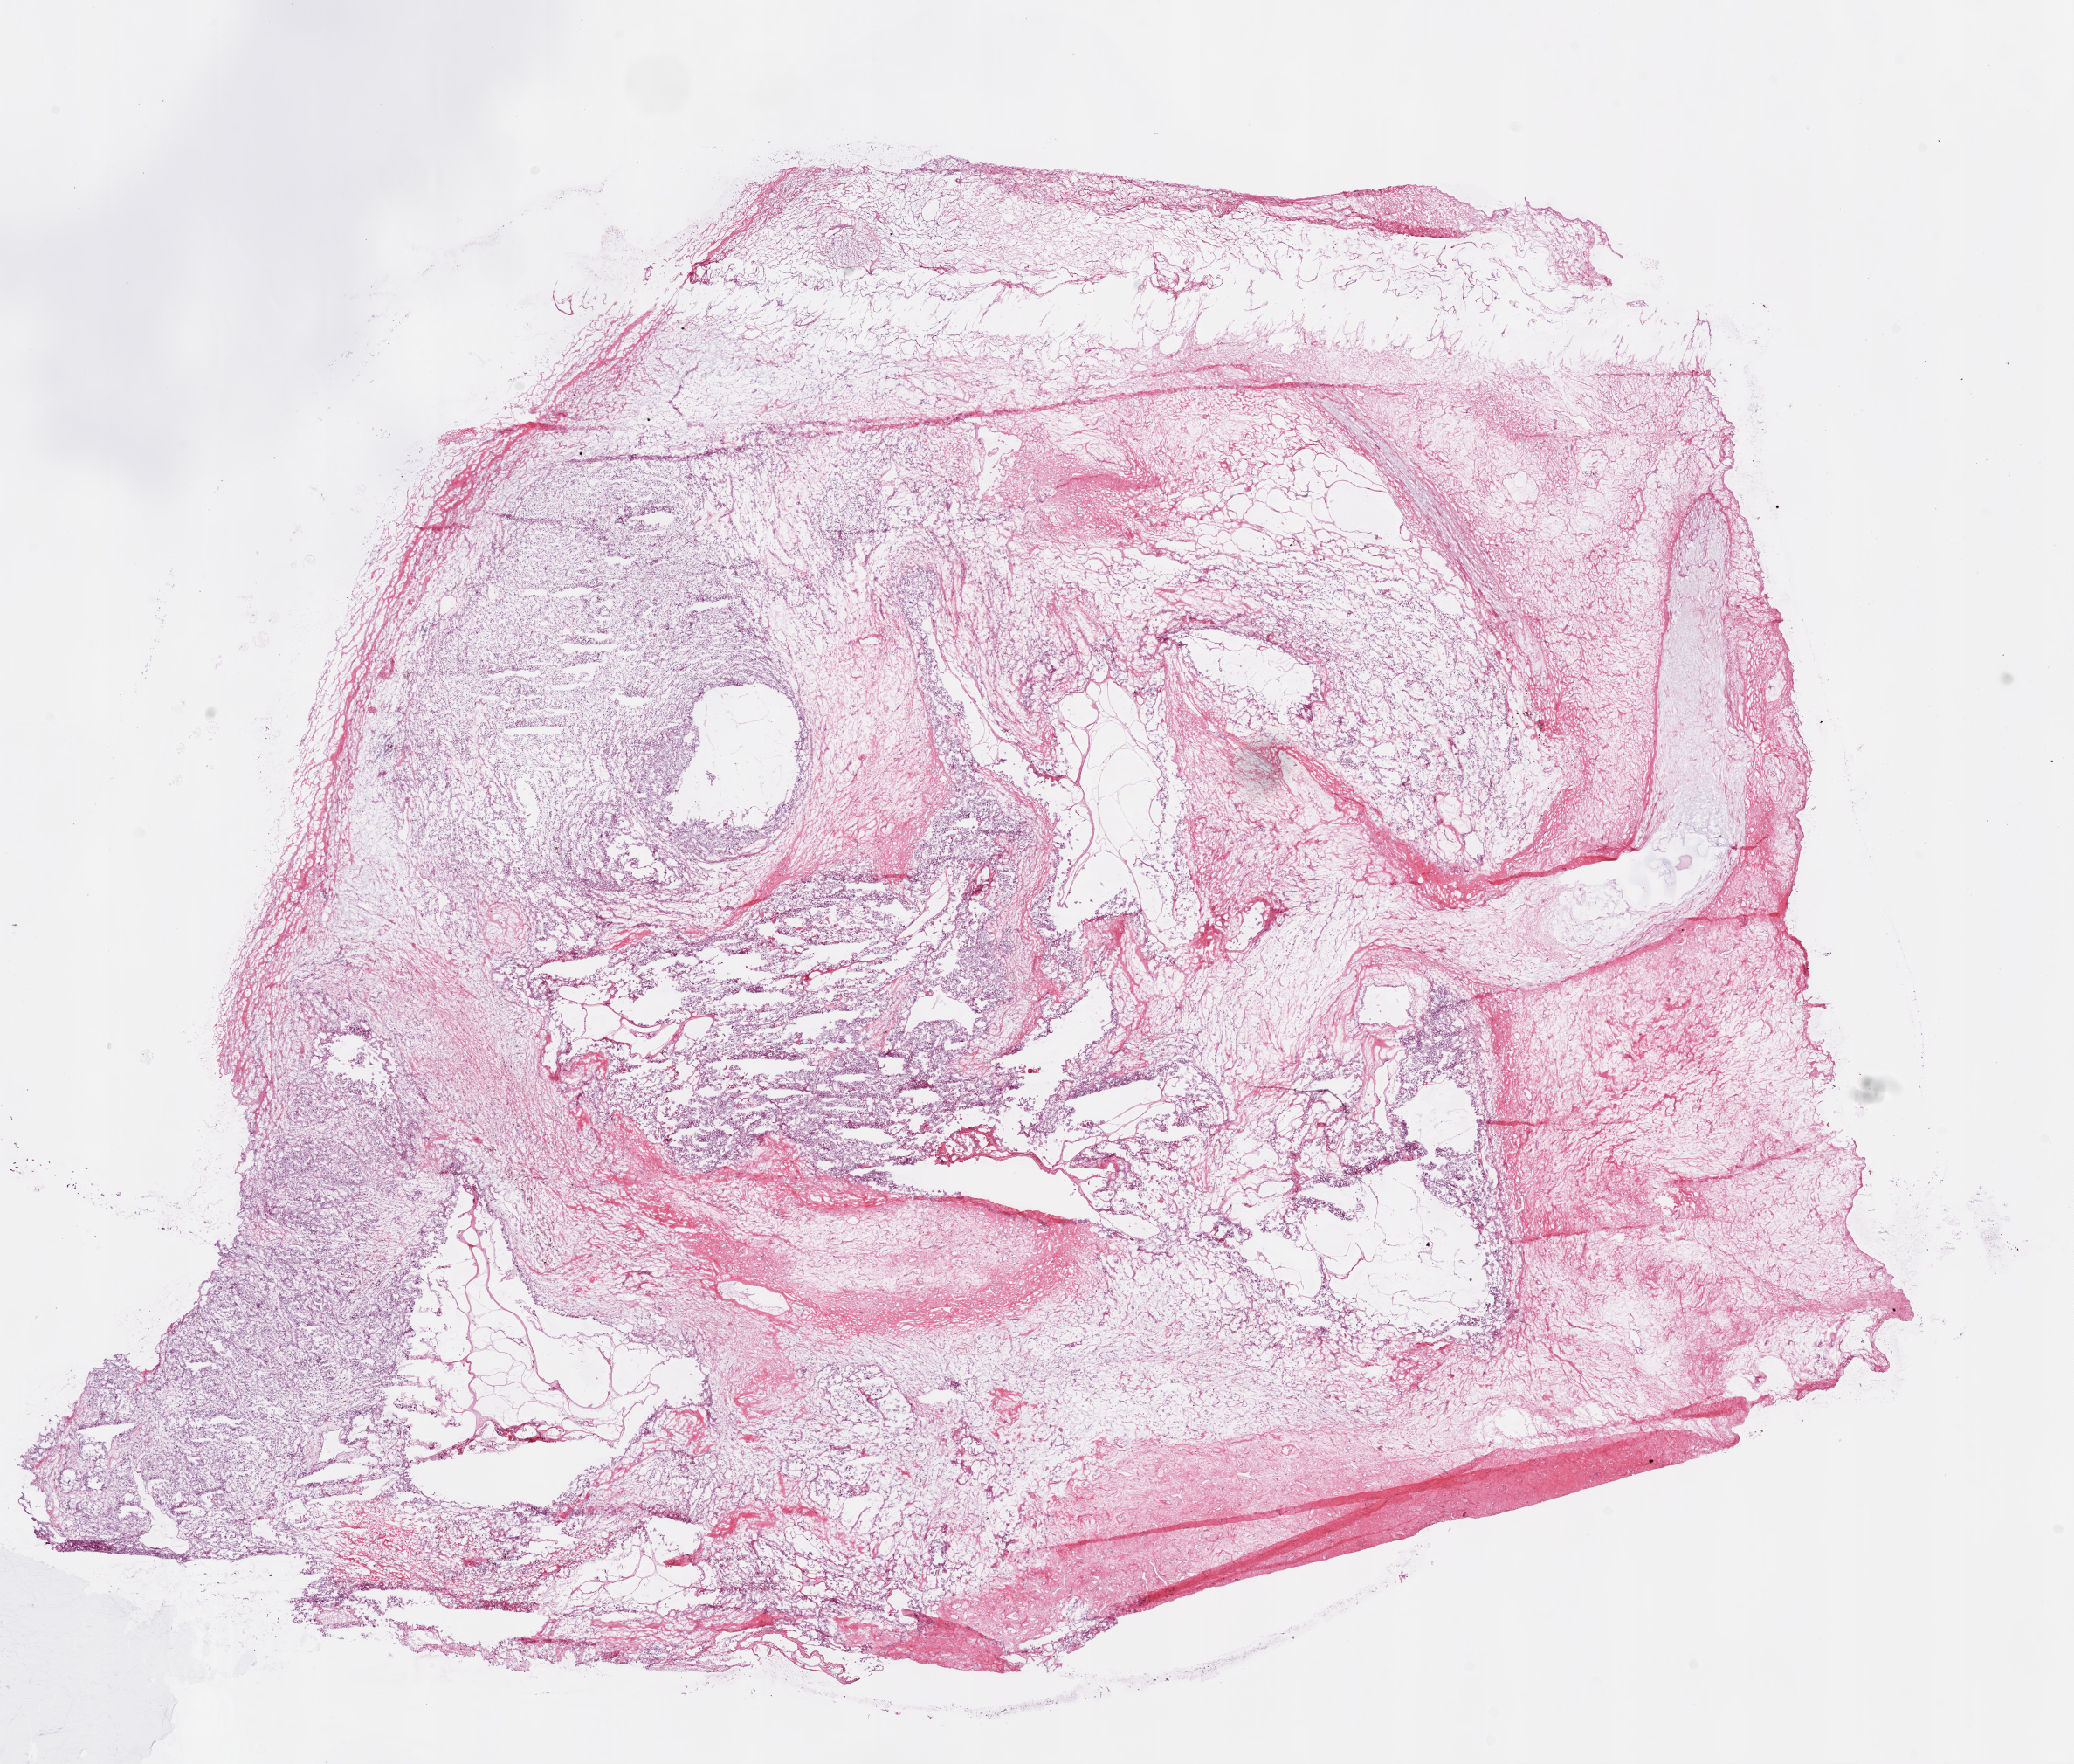
Digitized Hematoxylin and eosin (H&E) stained tissue section (whole slide), shown as a low-resolution overview of the whole scanned area (about 19.1 x 16.2 mm, from a 20x scan). Frozen section from the top of the tissue portion. Sample: primary tumour, kidney. Female patient; age at initial diagnosis 59 years. Histologic grade: G2 (moderately differentiated). Slide review estimates, as recorded: tumour cells 60%, tumour nuclei 80%, normal cells 0%, stromal cells 40%, necrosis 0%.
AJCC pathologic stage: III. Pathologic diagnosis: Clear cell adenocarcinoma, NOS. Laterality: right. TNM: T3b N0 M0.